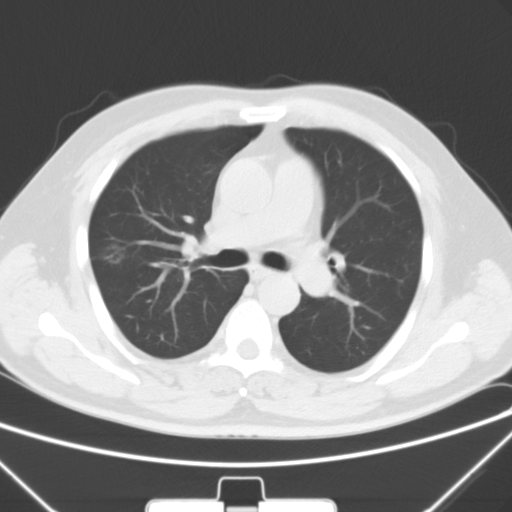
Chest CT, one axial slice; slice 39 of 64 in the series (ordered by position); 120 kVp; lung window (W 1500 / L -600 HU); 5 mm slice thickness; 512 × 512 image matrix, field of view 350 × 350 mm. Male patient, age 58 years. From the clinical record (not read from this slice): clinical TNM (as recorded): T1c N0 M0.
Structures marked on this image (bounding box drawn by a radiologist):
- lung tumour (recorded histology: adenocarcinoma): bounding box [x1, y1, x2, y2] px = [97, 240, 131, 271]